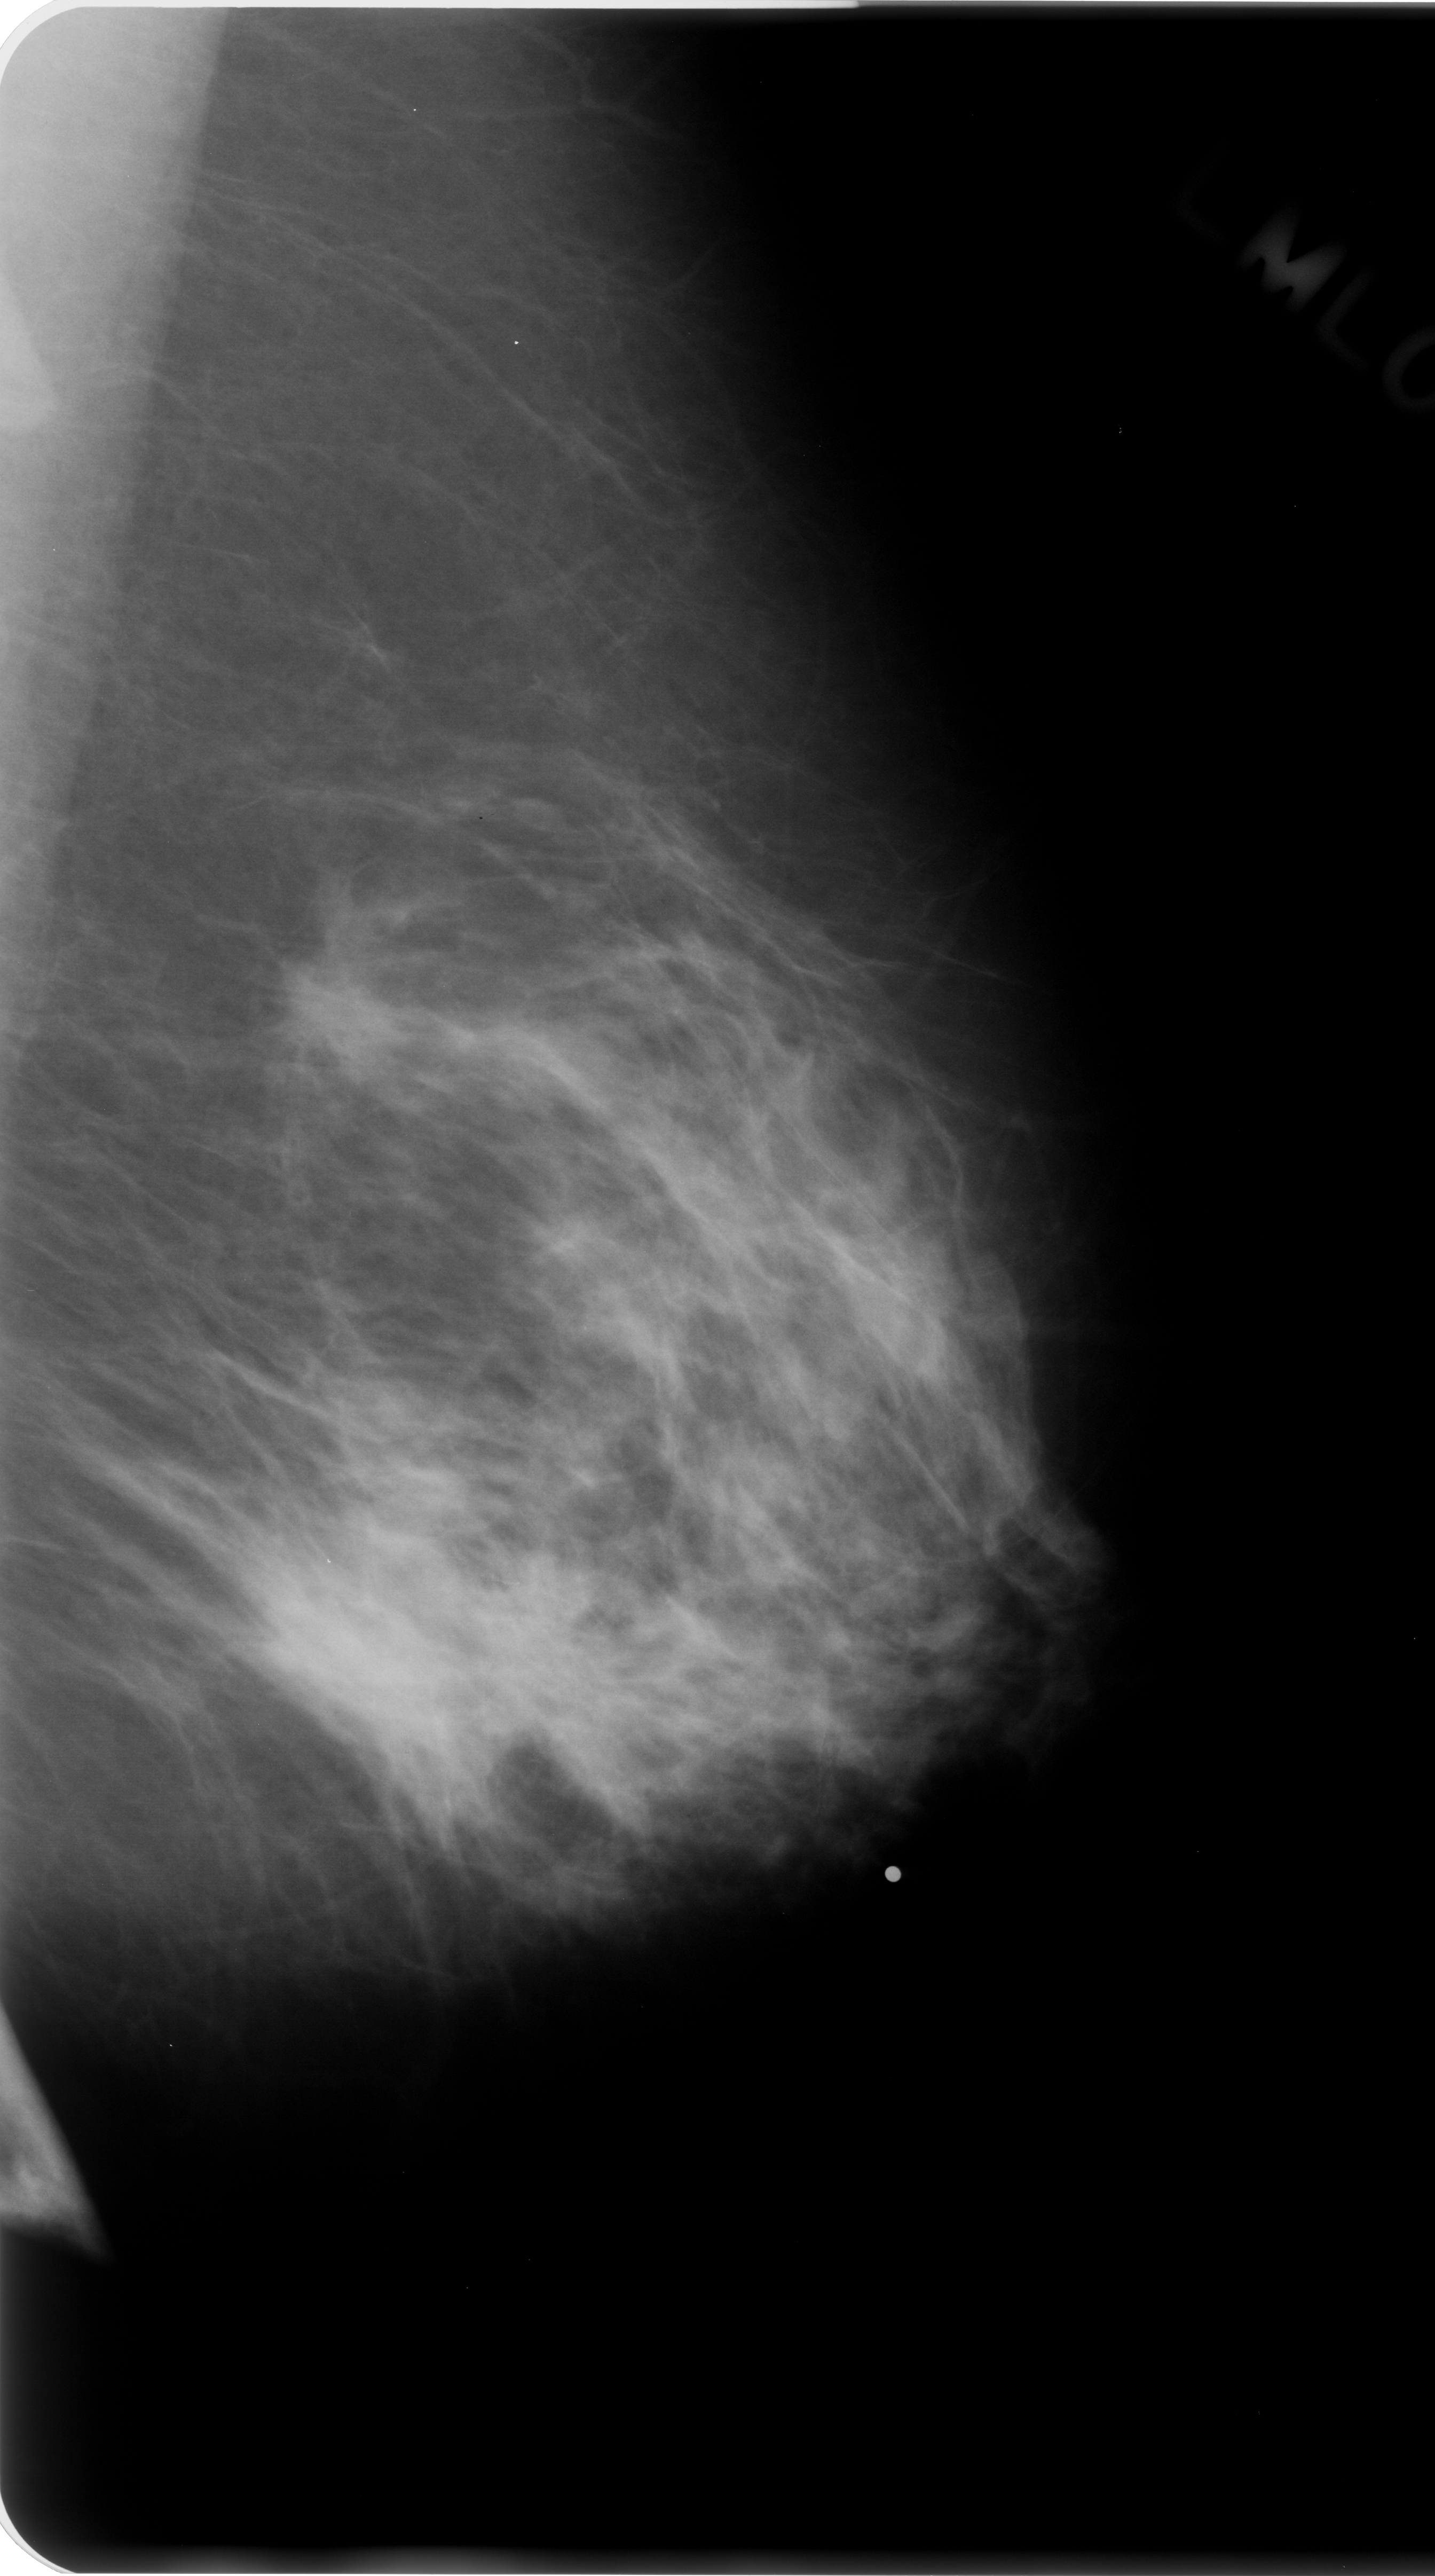
Digitized screen-film mammogram; left breast; mediolateral oblique (MLO) view; BI-RADS breast density category 2 (scale 1–4).
- Abnormality record for this image: Finding 1 of 2: mass, shape irregular, margins spiculated; BI-RADS assessment category 5; pathology (as recorded): malignant.
- Finding 2 of 2: mass, shape irregular, margins ill defined; BI-RADS assessment category 5; pathology (as recorded): malignant.